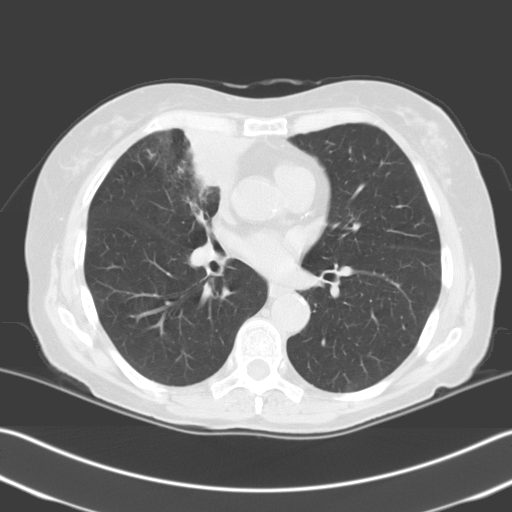
Low-dose screening chest CT, one axial slice. Position 114 of 204 along the scan axis. 140 kVp. Lung window (W 1500 / L -600 HU). 3.2 mm slice thickness. 512 × 512 image matrix, field of view 348 × 348 mm.
Outlined on this slice (manually delineated by an expert):
- lesion 1 (tumor, upper lobe of right lung): bounding box [x1, y1, x2, y2] px = [185, 131, 250, 192]